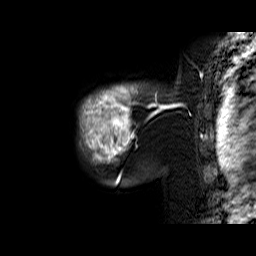
Breast MRI (dynamic contrast-enhanced), one sagittal slice. Position 53 of 60 along the scan axis. Dynamic contrast-enhanced series, time point 2 of 6 at this slice position (early post-contrast). 1.5 T. TE 6.4 ms, TR 32.9 ms. 256 × 256 image matrix, field of view 200 × 200 mm. Female patient. From the clinical record (not read from this slice): setting: breast cancer imaged before/during neoadjuvant chemotherapy; receptor status: triple-negative.
Outlined on this slice (semi-automatic segmentation, software-assisted and operator-edited):
- analysis volume of interest (the breast-tissue region the enhancement analysis was run in; not a lesion): bounding box [x1, y1, x2, y2] px = [80, 85, 159, 174]
- tumour enhancement mask (voxels above the 100 % enhancement threshold inside the analysis volume of interest): [80, 85, 159, 174]